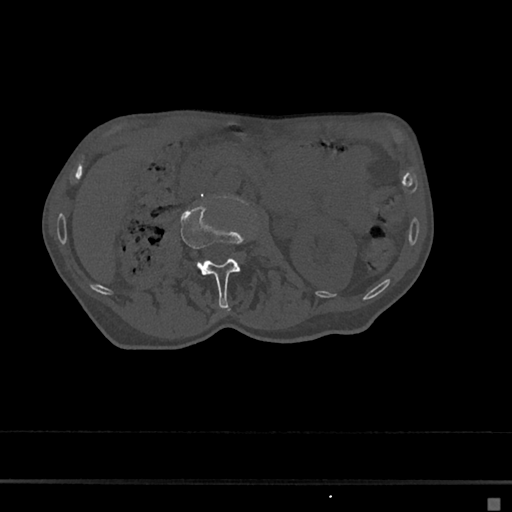
CT including the spine, one axial slice; 120 kVp; bone window (W 1800 / L 400 HU); 0.5 mm slice thickness; 512 × 512 image matrix. Patient: female, 68 years. From the clinical record (not read from this slice): primary cancer: renal.
Outlined on this slice (semi-automatically segmented with operator editing):
- L2 vertebra: bounding box <180,203,248,308> (left, top, right, bottom; pixels)